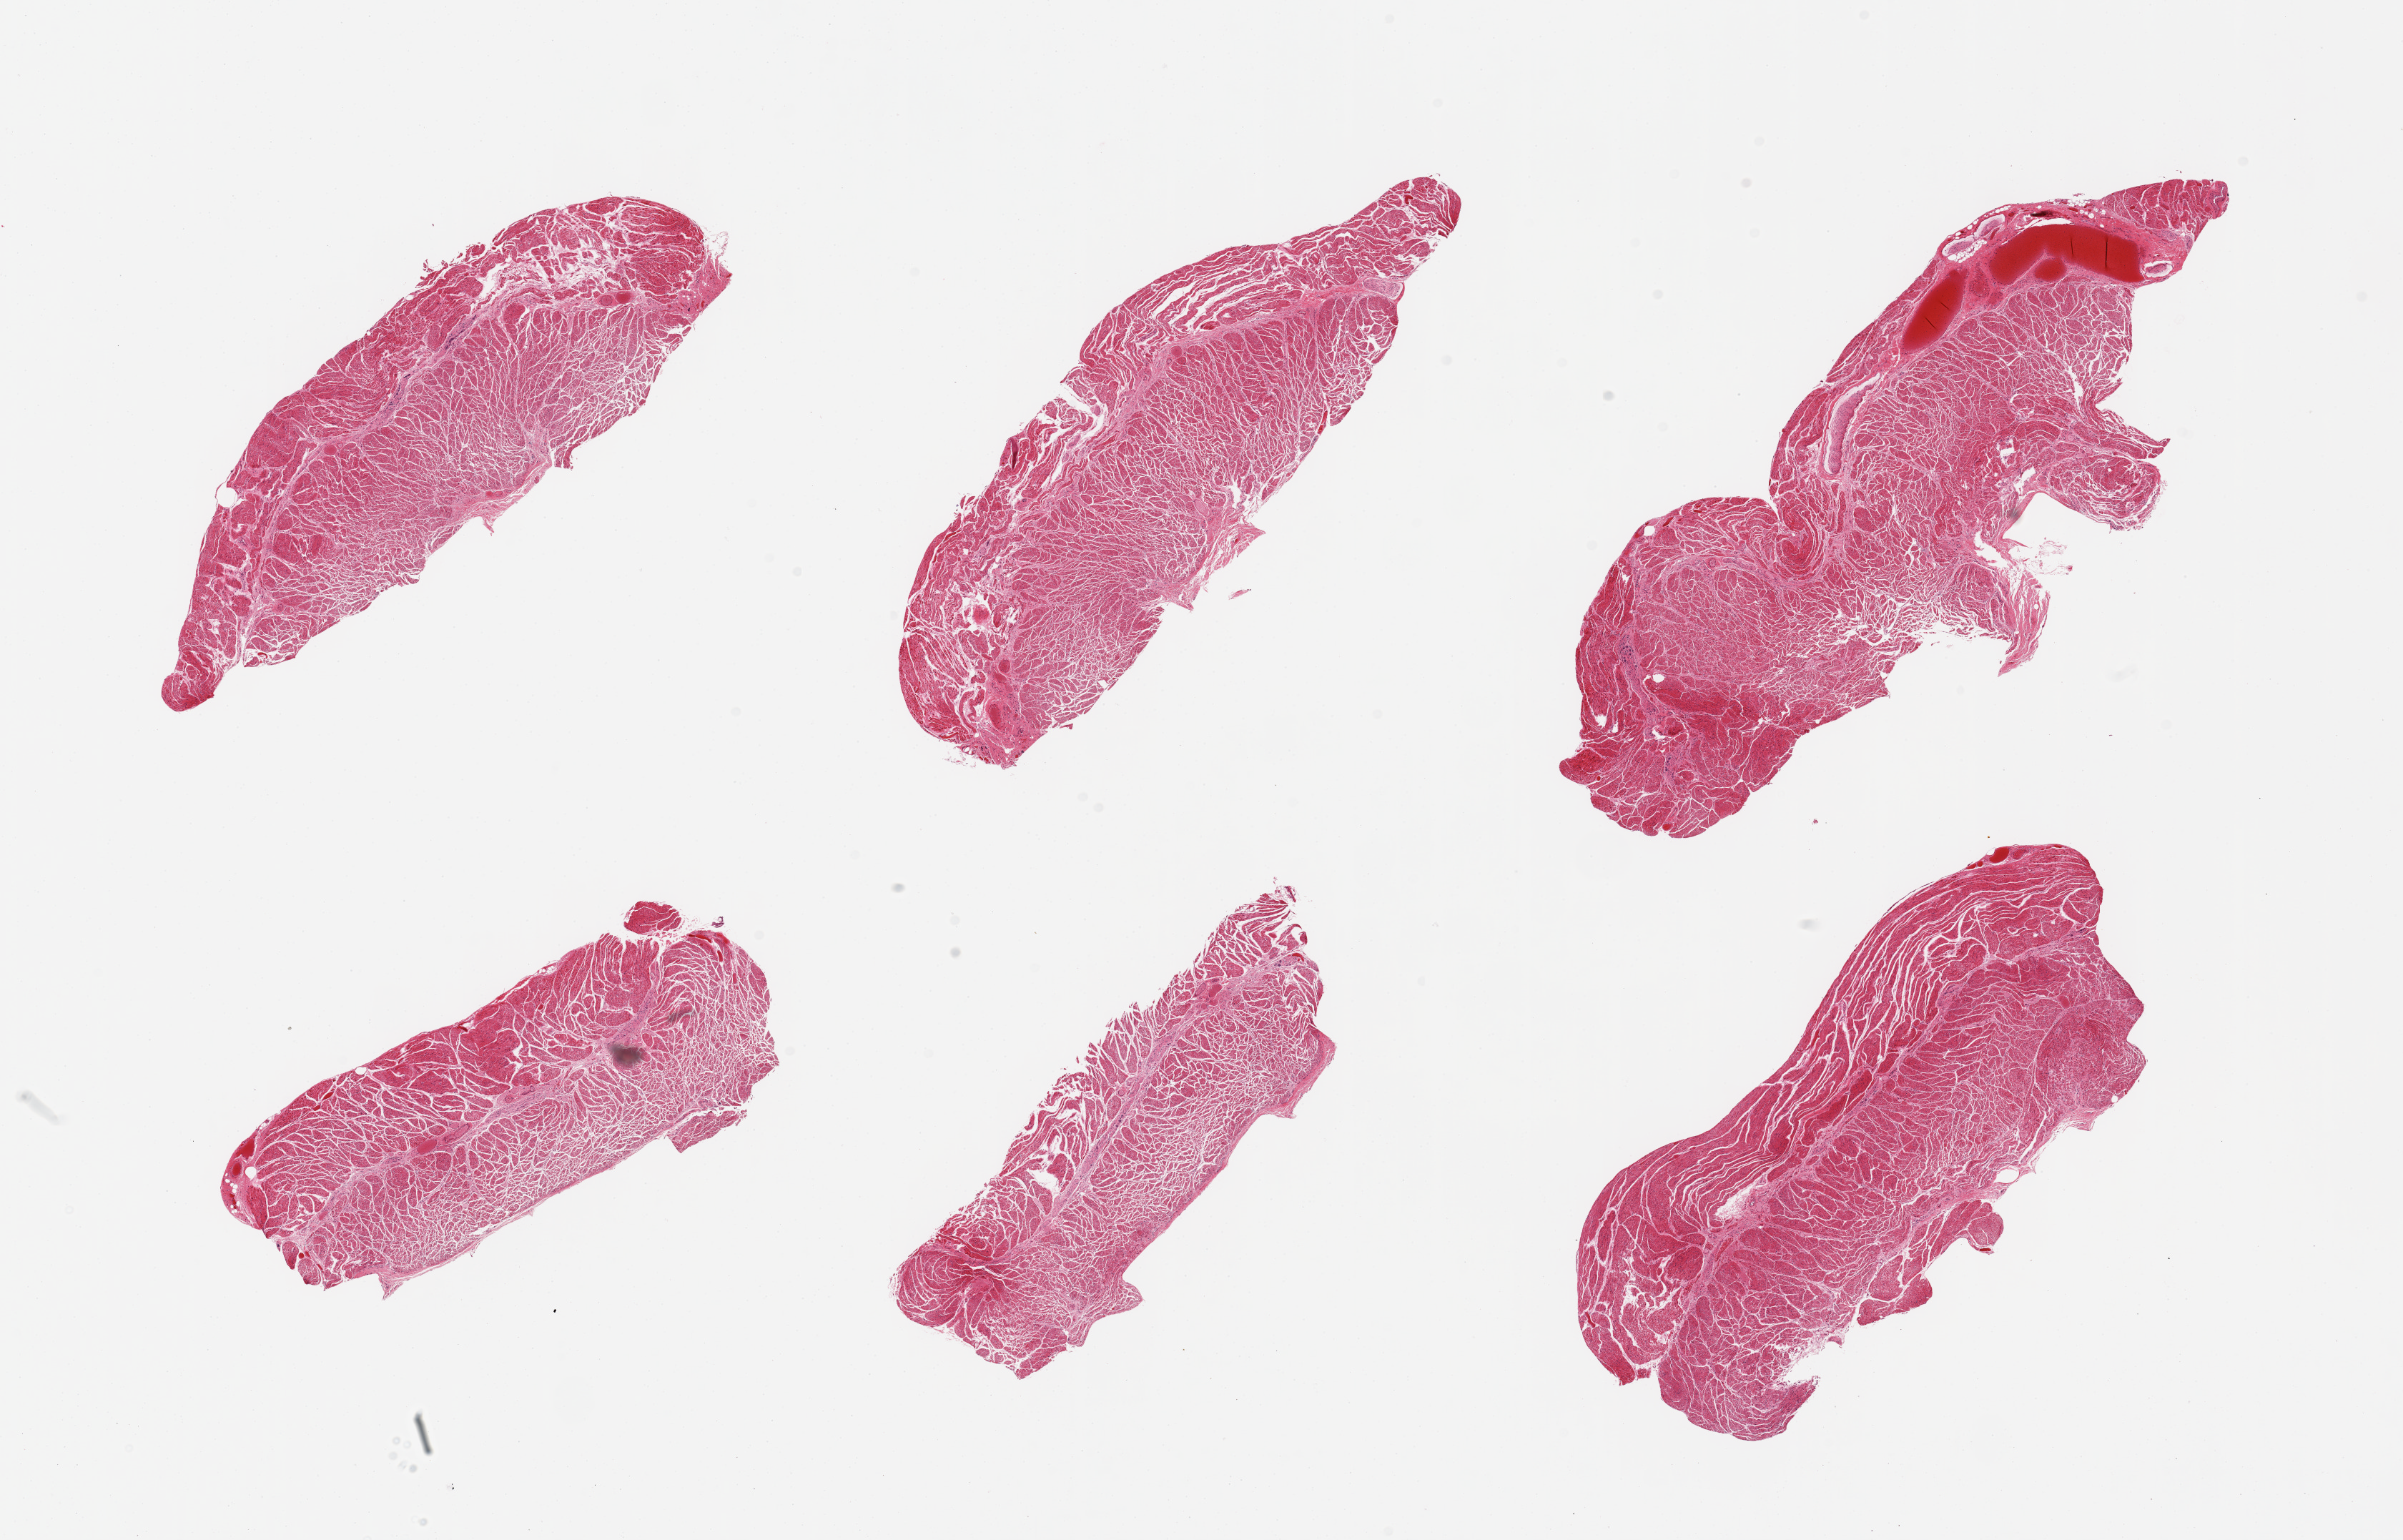
Haematoxylin and eosin whole-slide image — whole scanned area (about 26.6 x 17.0 mm, from a 20x scan) shown as a low-resolution overview, PAXgene-fixed, paraffin-embedded tissue, target tissue: esophageal muscle, donor tissue sample.
Pathologist's review note for this sample: 6 pieces; well trimmed.